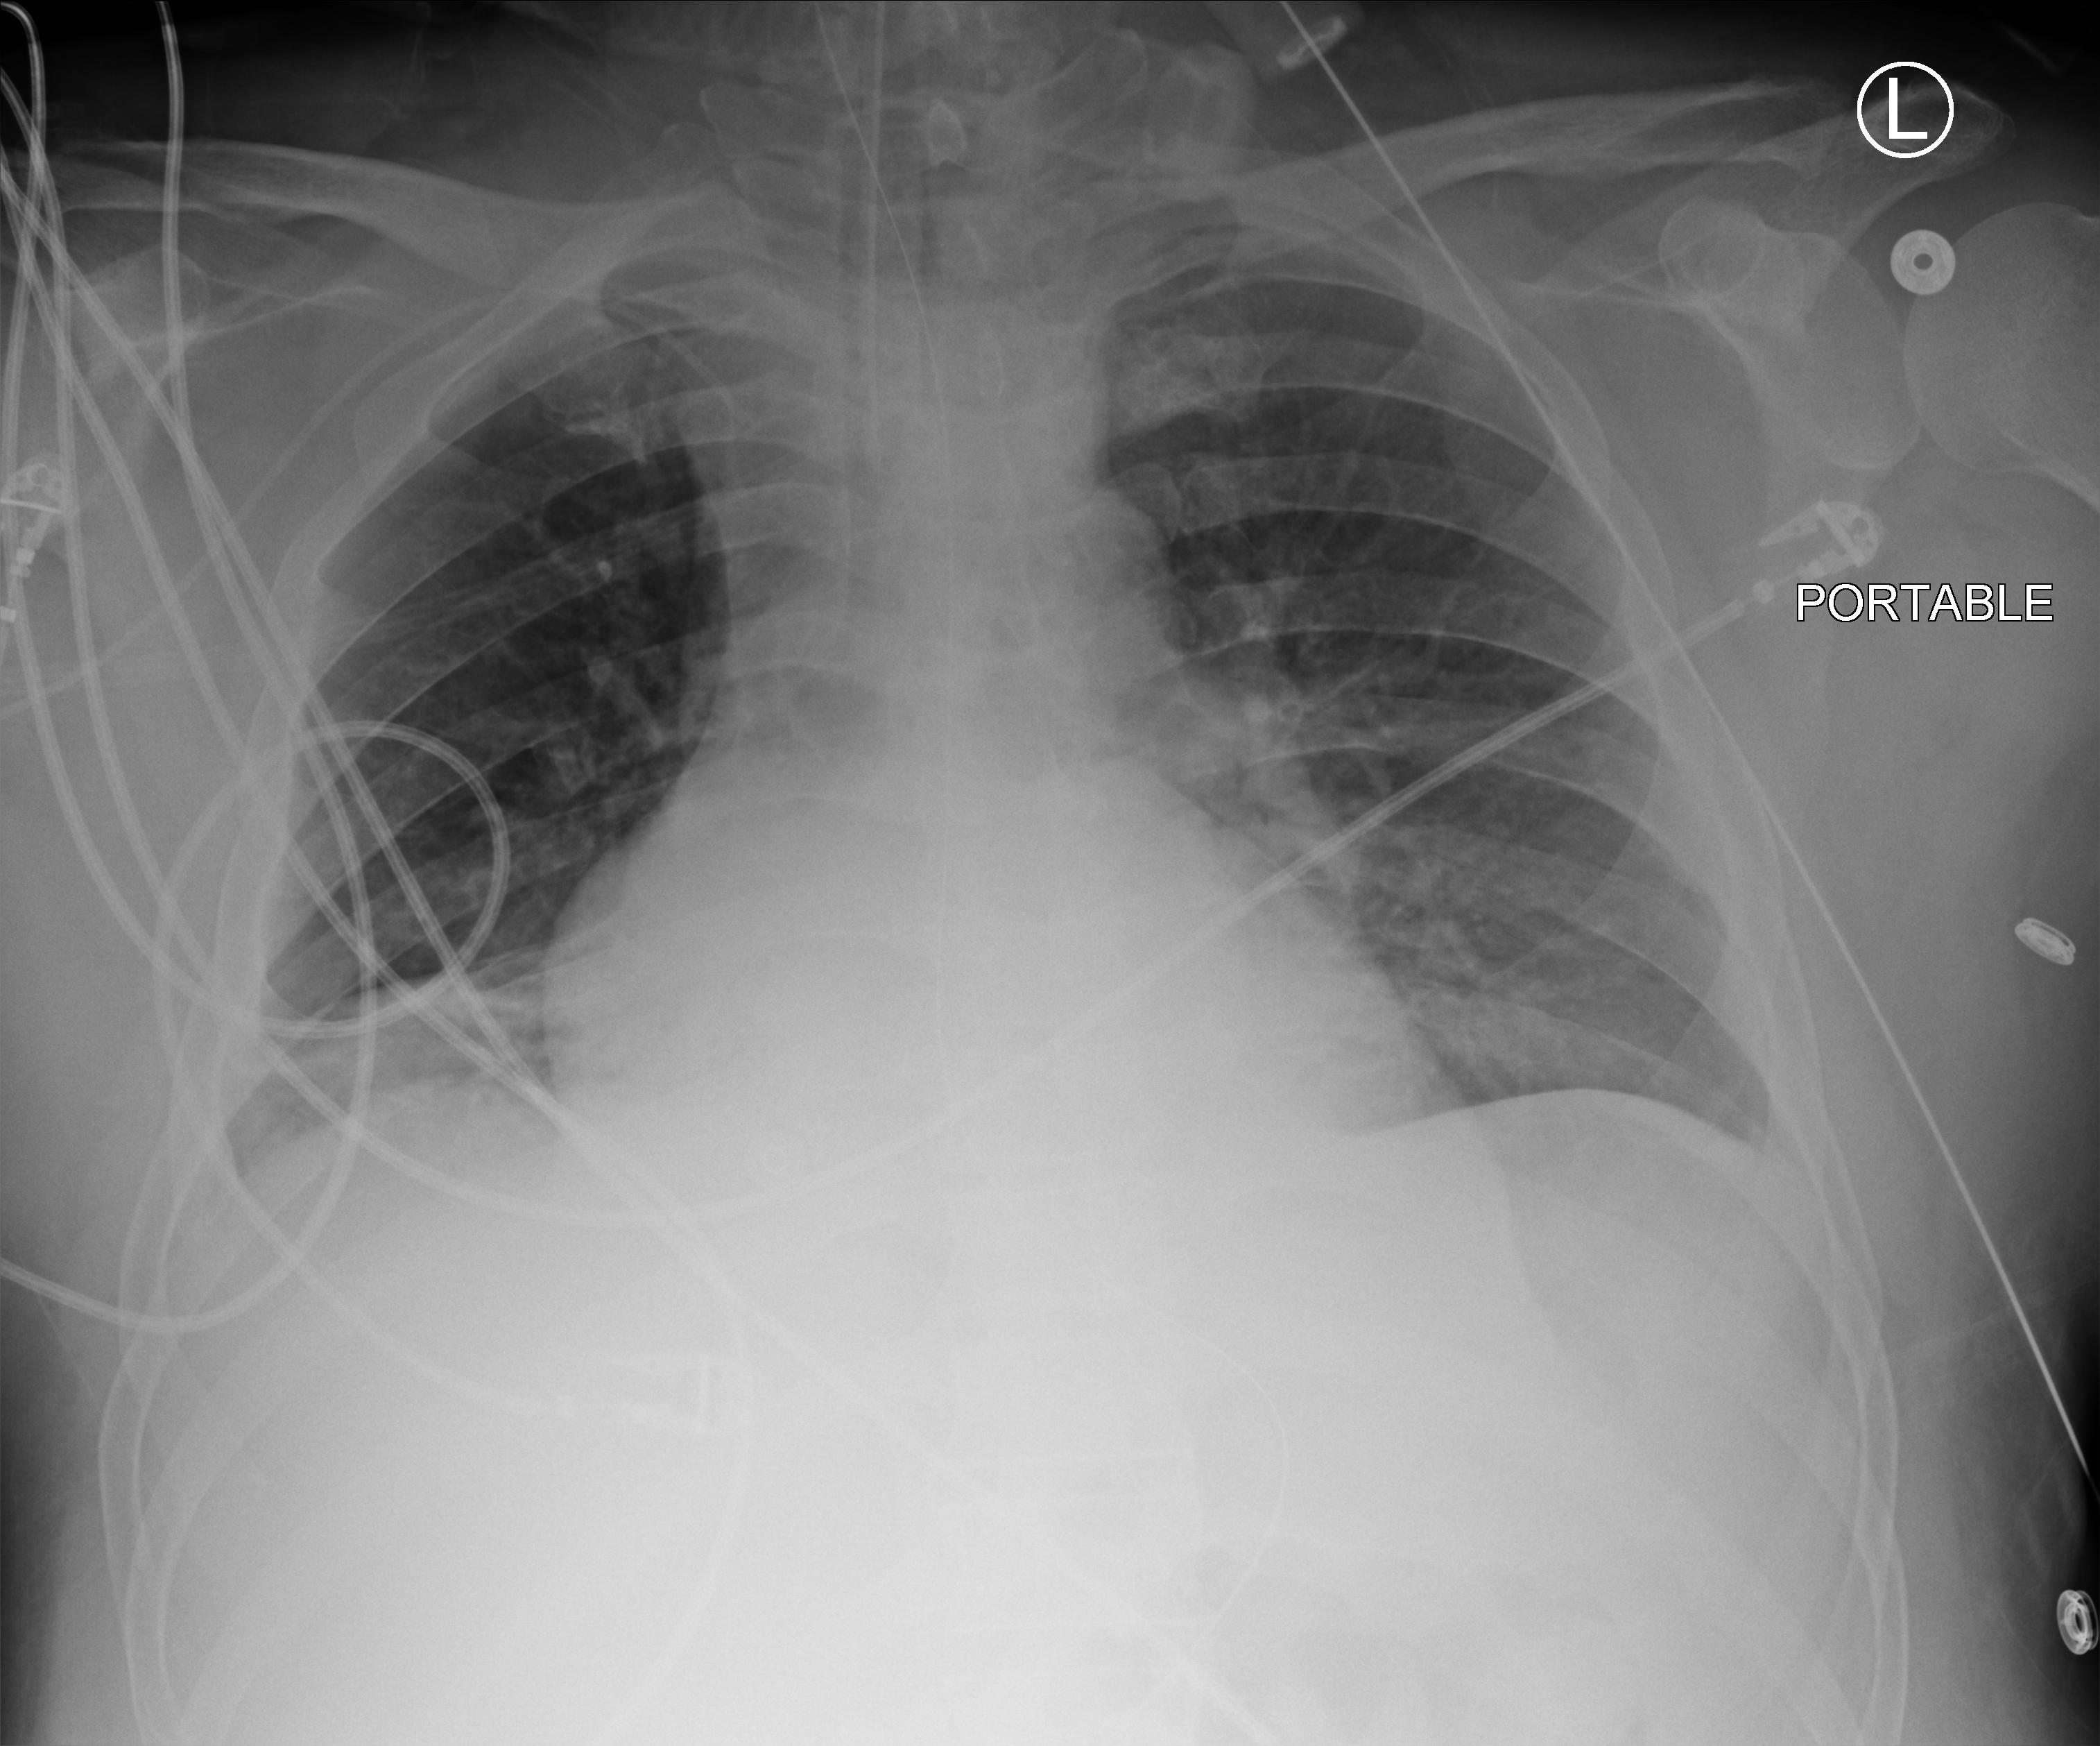
Chest X-ray (portable), anteroposterior (AP) projection. Patient hospitalised with COVID-19; male, aged 18–59 years.
Hospital-stay facts (about this admission, not read from this image; timing relative to this image not recorded): length of hospital stay: 65 days; admitted to intensive care during this hospital stay: yes; mechanically ventilated during this hospital stay: yes.